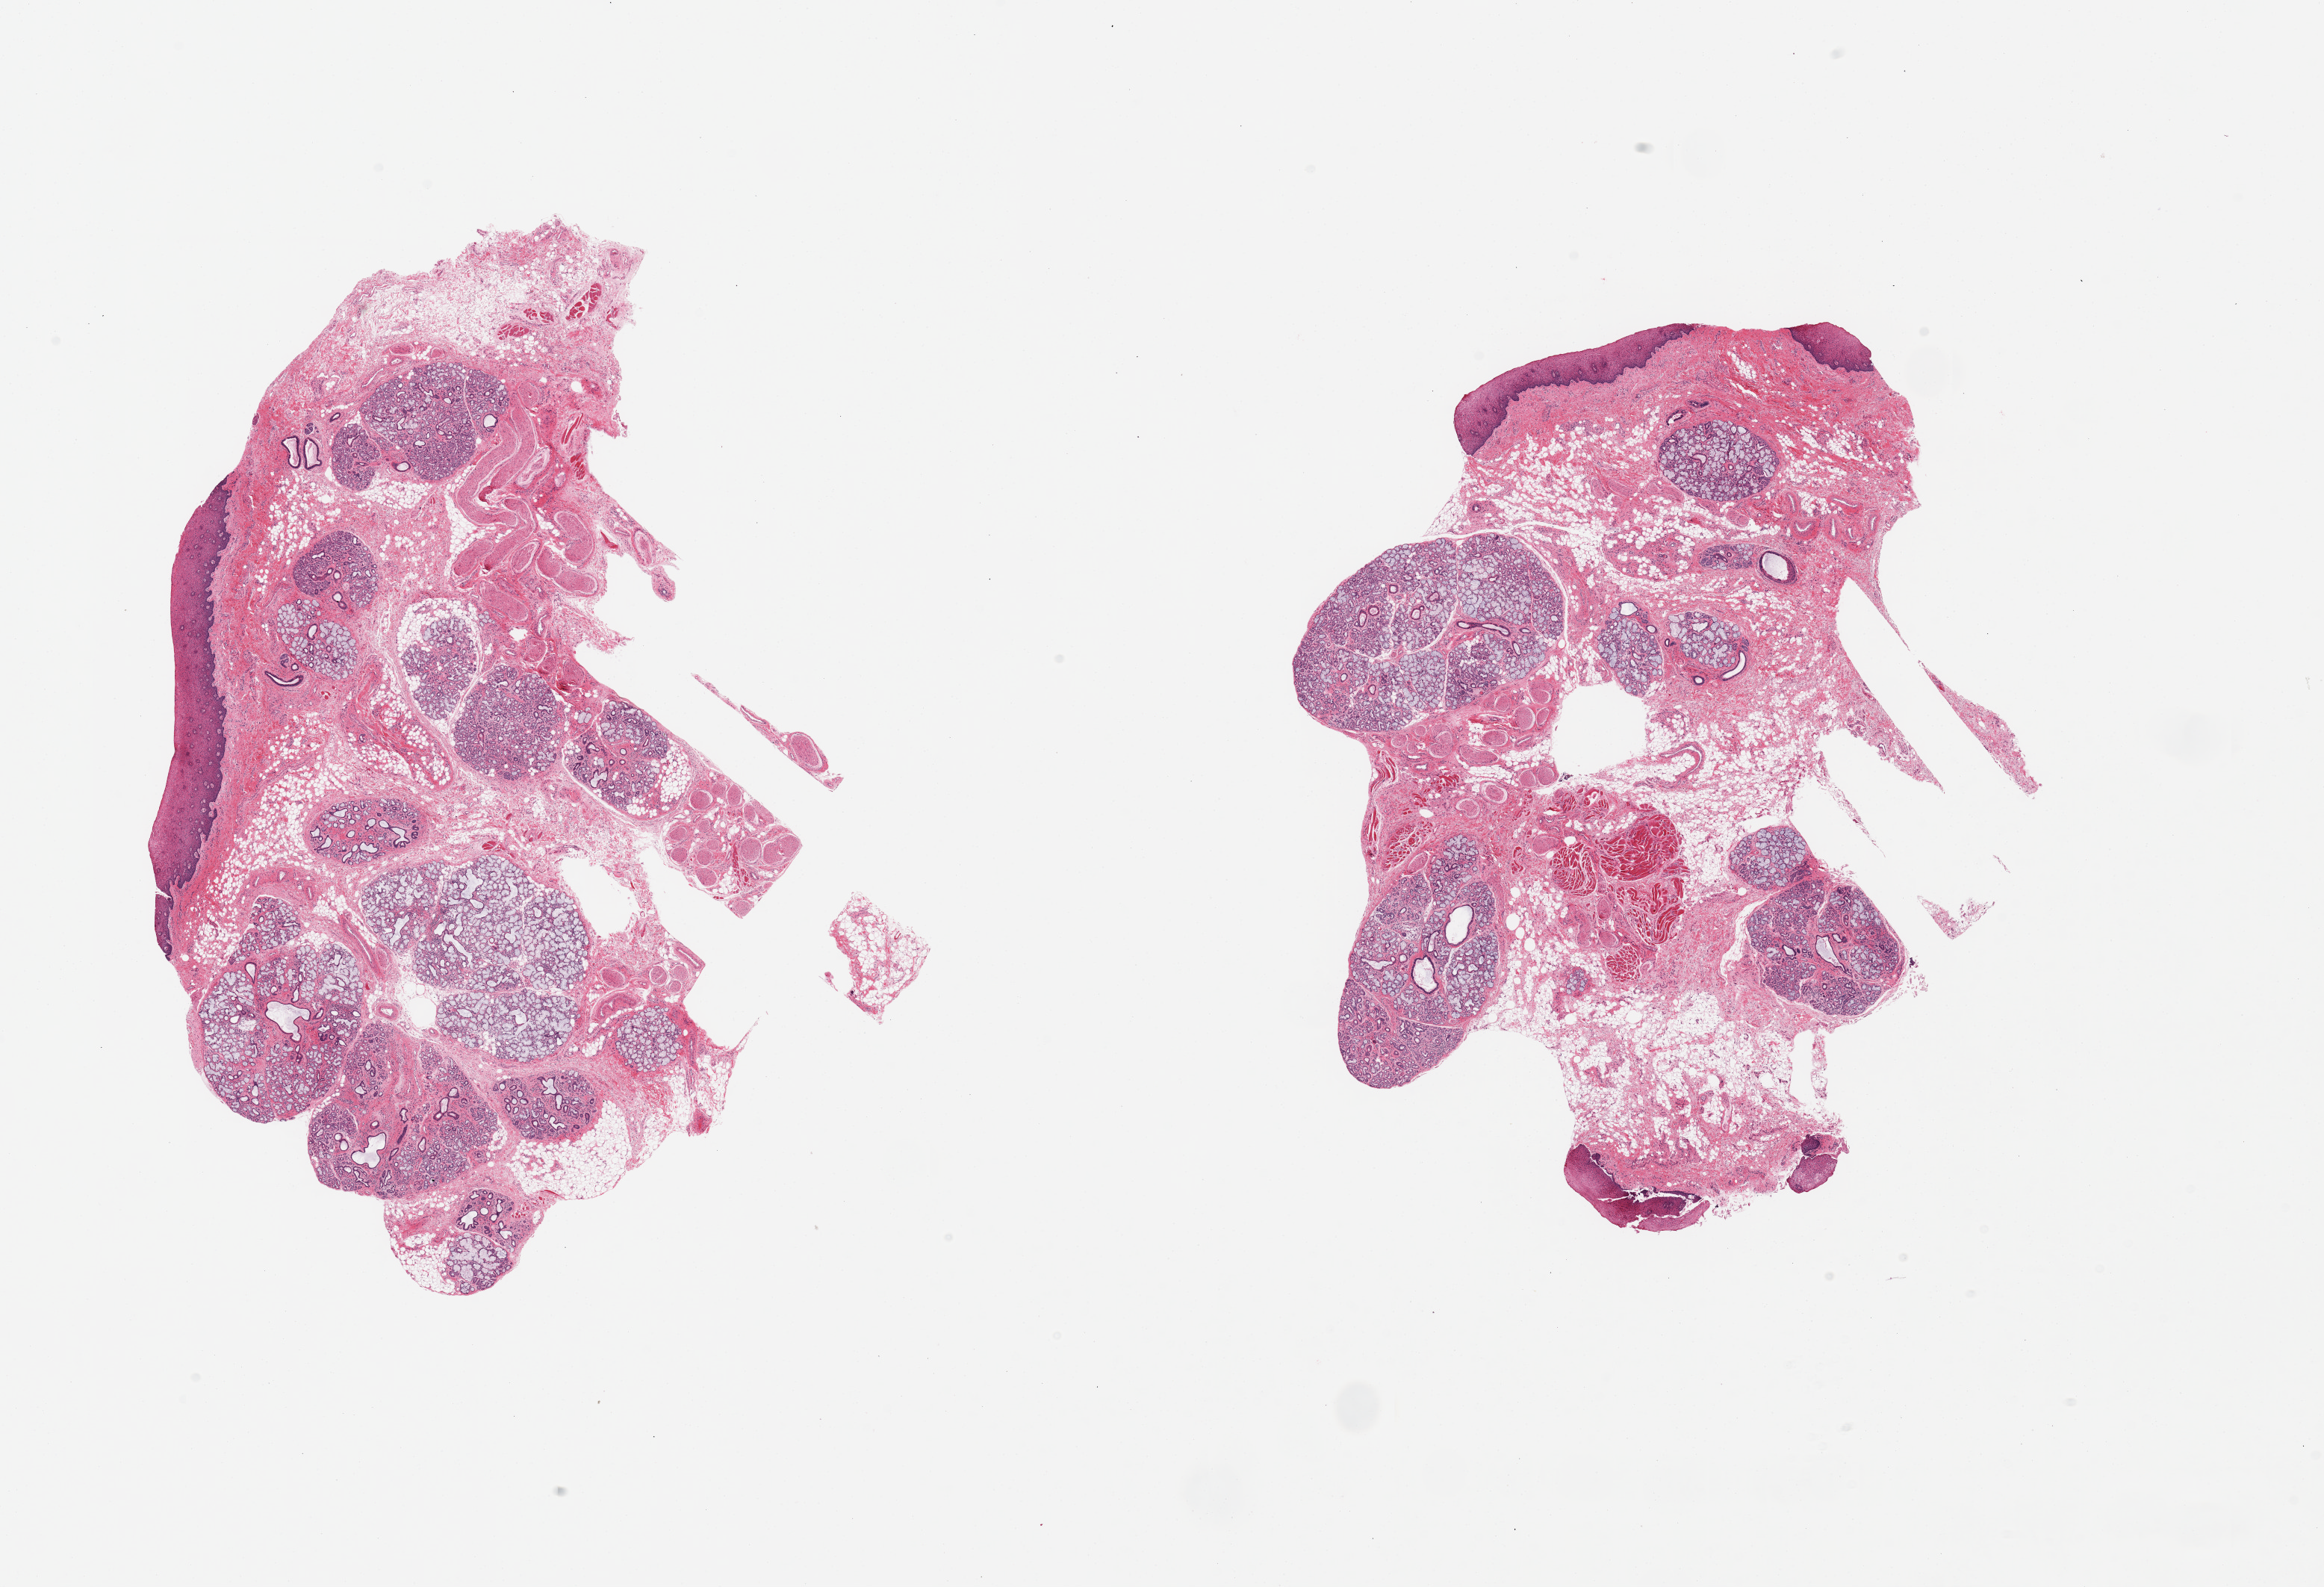
Digitized hematoxylin and eosin (H&E)-stained section, brightfield, low-resolution overview of the scanned area, about 24.6 x 16.8 mm (from a 20x scan). Male donor.
- specimen: PAXgene-fixed paraffin-embedded (PFPE) section; target tissue: minor salivary gland; donor tissue sample